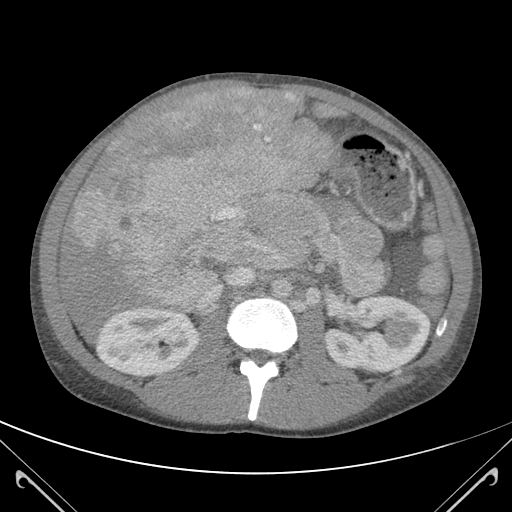
Contrast-enhanced abdominal CT (liver protocol), one axial slice. Position 59 of 118 along the scan axis. 120 kVp. Soft-tissue window (W 400 / L 40 HU). 512 × 512 image matrix. From the clinical record (not read from this slice): diagnosis: hepatocellular carcinoma (patient treated with transarterial chemoembolisation; whether this scan precedes or follows treatment is not stated here); TNM stage (as recorded): Stage-IIIB; Child-Pugh class: A.
Outlined on this slice (semi-automatic segmentation, software-assisted and operator-edited):
- abdominal aorta: bounding box (x1, y1, x2, y2) in pixels: (272, 279, 290, 299)
- liver parenchyma outside the tumour (the mass and vessels are separate outlines, so this box may not span the whole liver): (58, 88, 337, 338)
- mass: (71, 89, 328, 315)
- liver vessels: (202, 235, 262, 302)